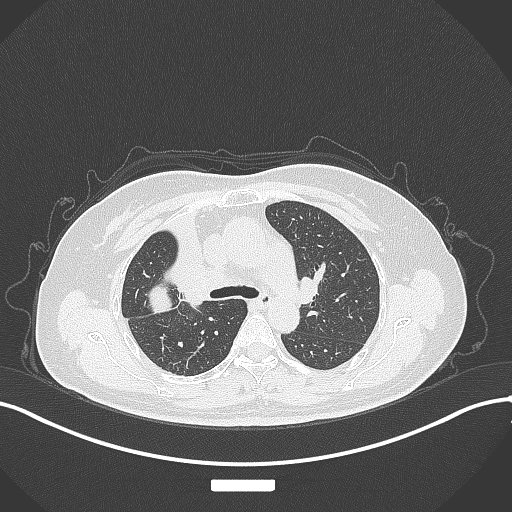
Chest CT, one axial slice; 120 kVp; lung window (W 1500 / L -600 HU); 1 mm slice thickness; 512 × 512 image matrix. Patient: female, 60 years. Case-level facts recorded for this patient, not image findings: clinical TNM (as recorded): T3 N1 M1.
Annotated regions visible in this slice (rectangle marked by the reading radiologist):
- lung tumour (recorded histology: adenocarcinoma): bounding box <136,282,183,323> (left, top, right, bottom; pixels)